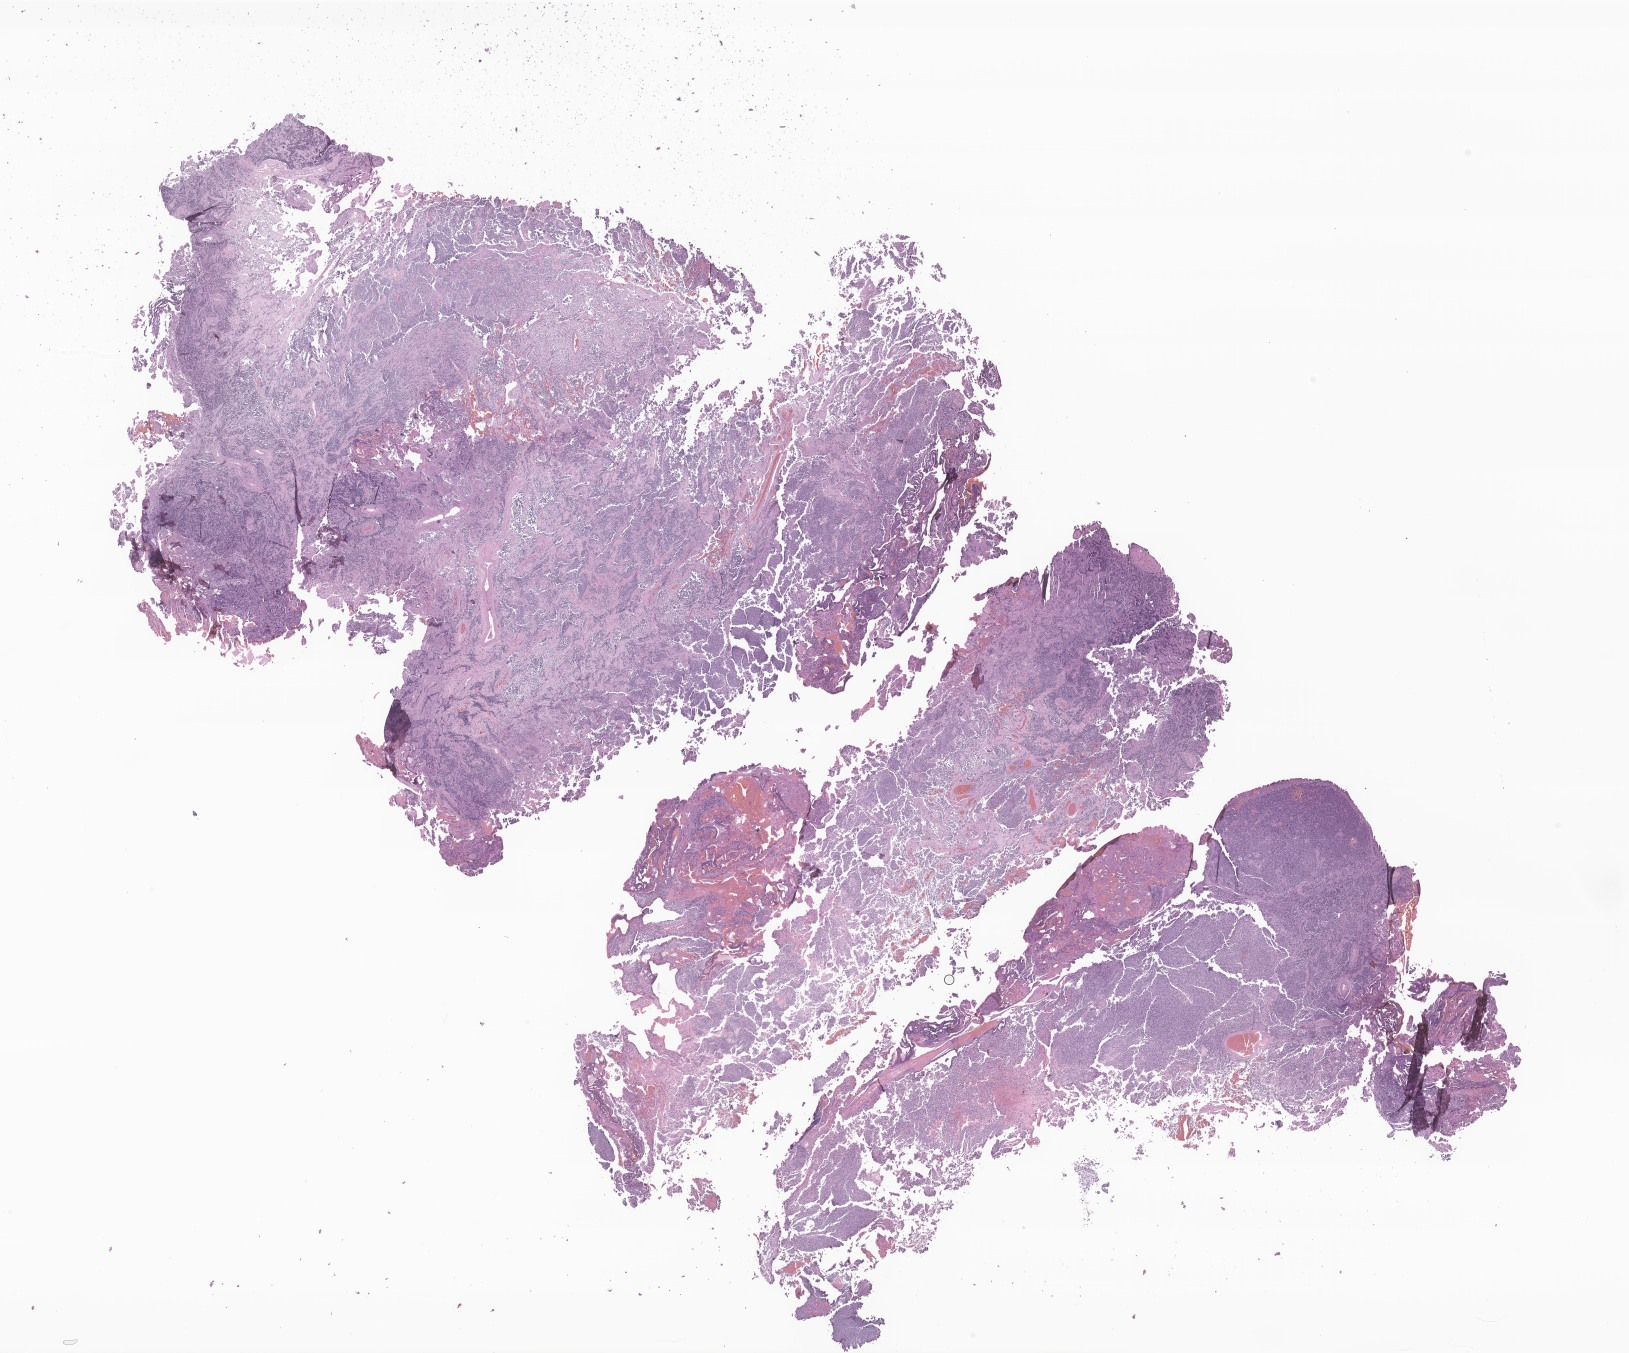
Digitized haematoxylin and eosin-stained section of tumor tissue from the brain, whole scanned area (about 27.5 x 22.8 mm) shown as a low-resolution overview. Formalin-fixed paraffin-embedded section. Patient female; age 133 months.
• recorded diagnosis: Medulloblastoma, NOS